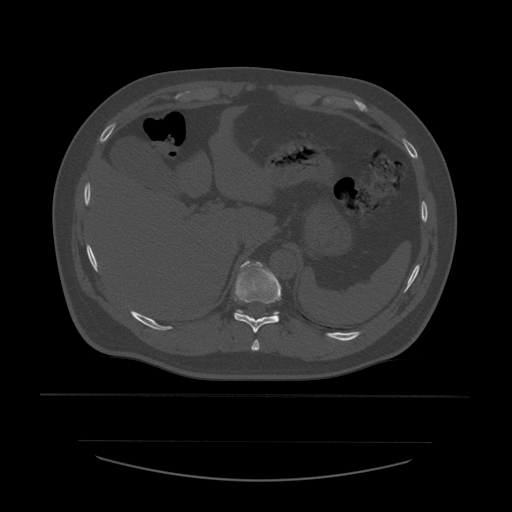
CT including the spine, one axial slice; reconstruction kernel STANDARD; 120 kVp; bone window (W 1800 / L 400 HU); 512 × 512 image matrix, field of view 441 × 441 mm. Patient age 44 years. Case-level facts recorded for this patient, not image findings: primary cancer: soft tissue sarcoma.
Structures marked on this image (semi-automatic segmentation, software-assisted and operator-edited):
- T10 vertebra: bounding box <234,261,282,333> (left, top, right, bottom; pixels)
- T11 vertebra: <237,262,280,315>
- T9 vertebra: <251,340,260,351>